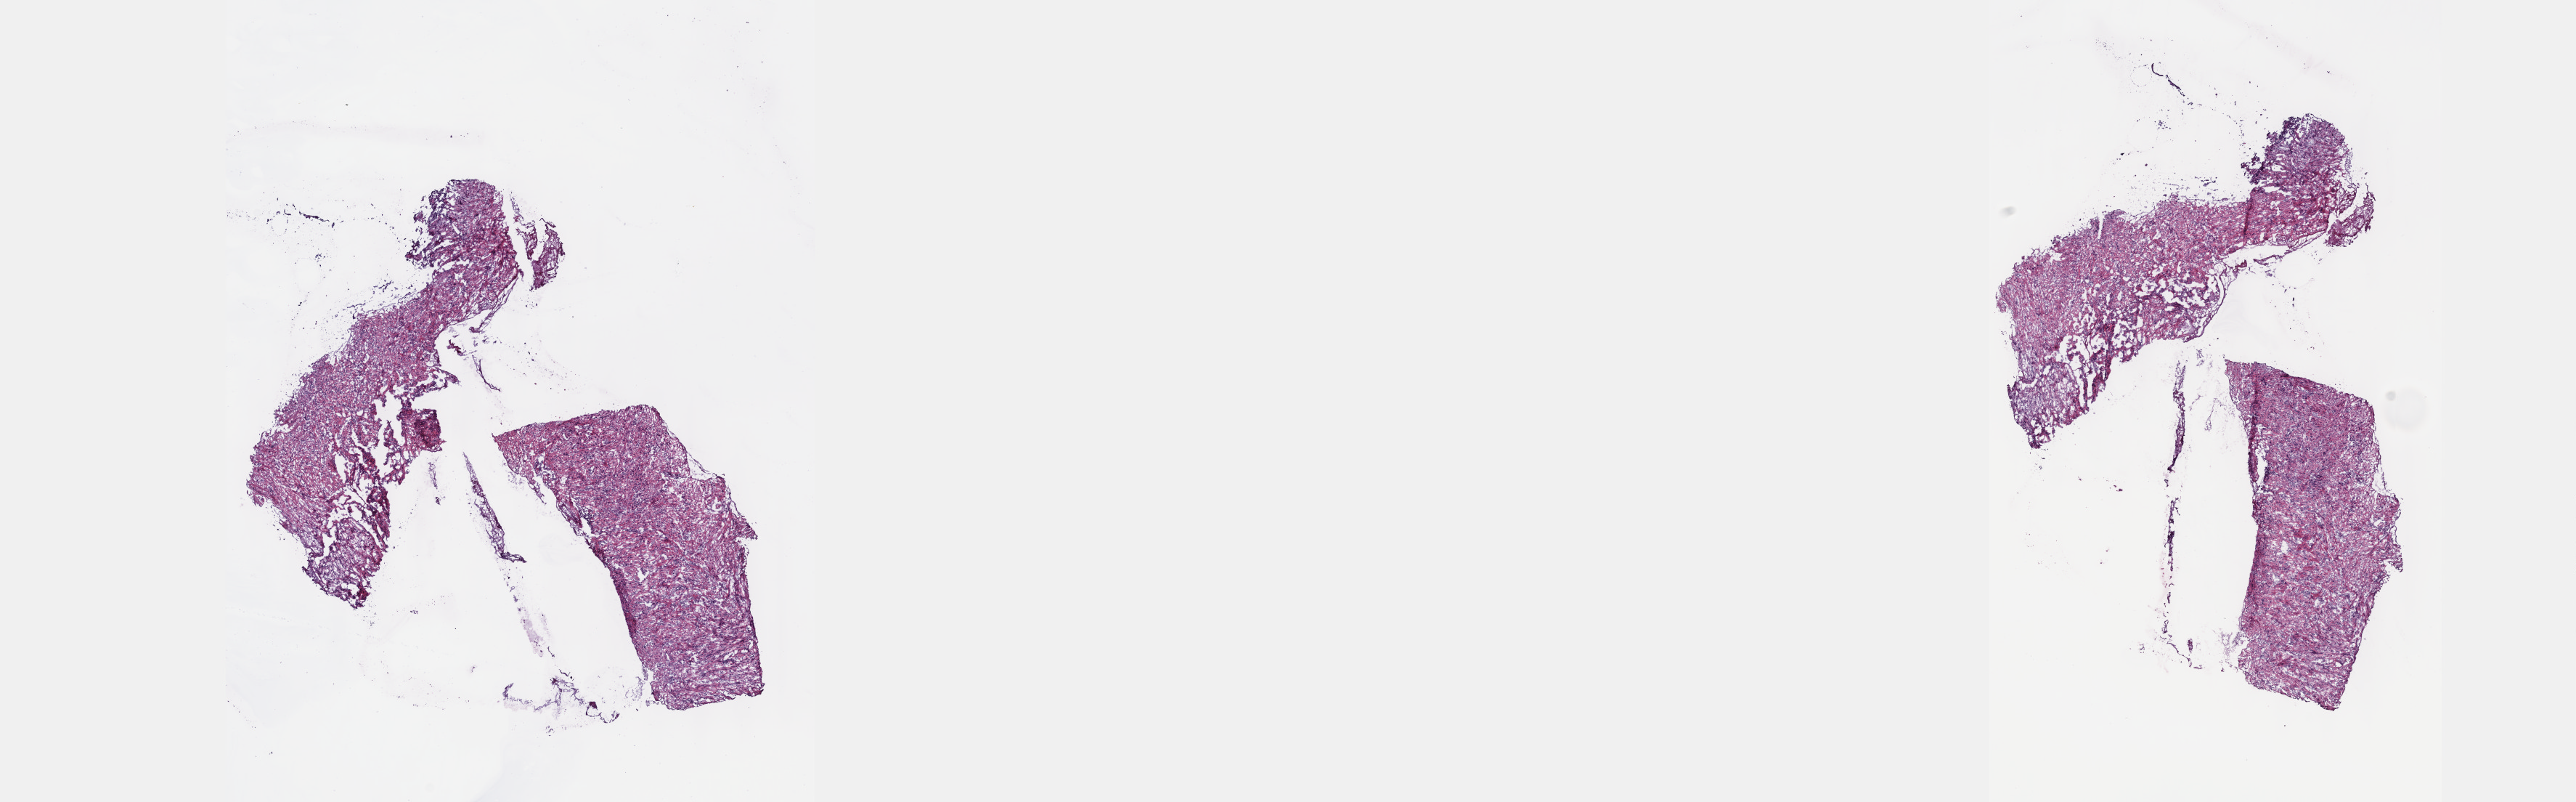
Digitized H&E-stained tissue section (whole slide), shown as a low-resolution overview of the whole scanned area (about 28.7 x 8.9 mm, acquisition: 40x scan), frozen section, primary tumour sample from the mesothelium. Patient: female, age at initial diagnosis 81 years. Pathologist review of this section (percent, as recorded): tumour cells 60%, tumour nuclei 60%, normal cells 0%, stromal cells 40%, necrosis 0%. Infiltration values recorded for this section: lymphocyte infiltration 4%, monocyte infiltration 1%, neutrophil infiltration 4%.
- AJCC pathologic stage: I (7th edition)
- diagnosis: Epithelioid mesothelioma, malignant
- laterality: right